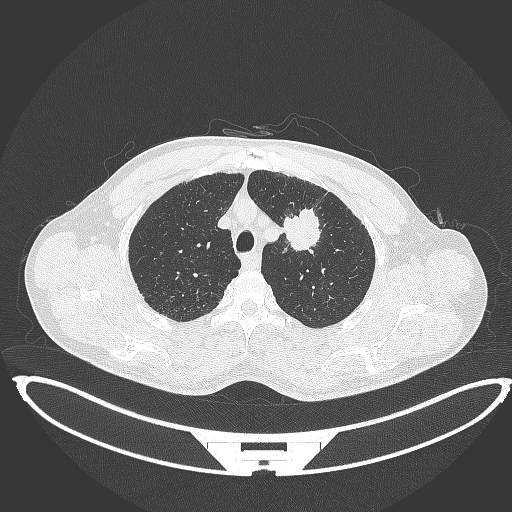
Chest CT, one axial slice; position 353 of 395 along the scan axis; 120 kVp; lung window (W 1500 / L -600 HU); 1 mm slice thickness; 512 × 512 image matrix. Male patient, age 60 years. Case-level facts recorded for this patient, not image findings: clinical TNM (as recorded): T2a N0 M0.
Annotated regions visible in this slice (rectangle marked by the reading radiologist):
- lung tumour (recorded histology: squamous cell carcinoma): bounding box <278,201,322,251> (left, top, right, bottom; pixels)